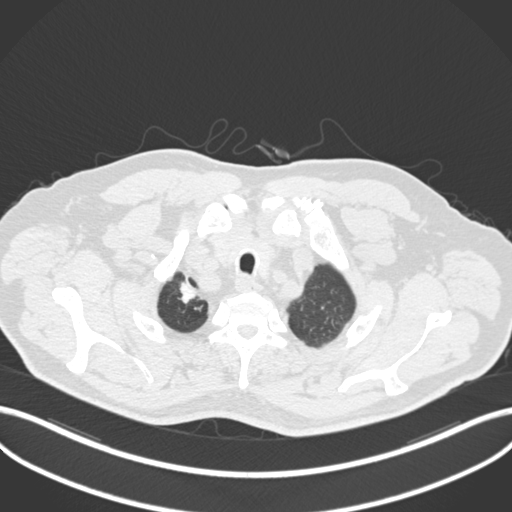
Chest CT, one axial slice. Position 187 of 255 along the scan axis. Reconstruction kernel B30f. 120 kVp. Lung window (W 1500 / L -600 HU). 512 × 512 image matrix, field of view 400 × 400 mm. Male patient, age 60 years. Case-level facts recorded for this patient, not image findings: clinical TNM (as recorded): T1b N1 M0.
Annotated regions visible in this slice (rectangle marked by the reading radiologist):
- lung tumour (recorded histology: squamous cell carcinoma): box from (x=173, y=275) to (x=201, y=310) px